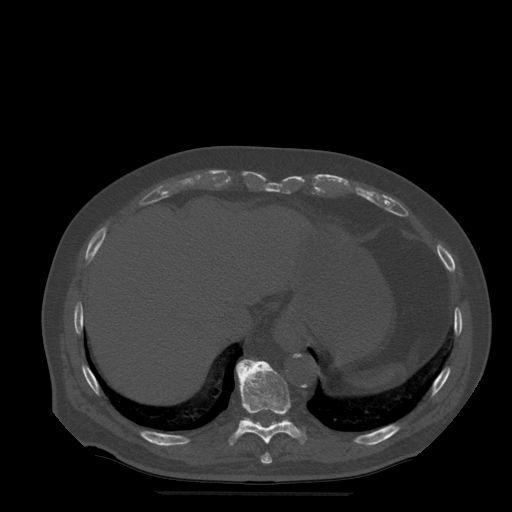
CT including the spine, one axial slice; position 265 of 522 along the scan axis; bone window (W 1800 / L 400 HU); 1.25 mm slice thickness; 512 × 512 image matrix, field of view 420 × 420 mm. Patient age 72 years. Case-level facts recorded for this patient, not image findings: primary cancer: prostate.
Outlined on this slice (semi-automatic segmentation, software-assisted and operator-edited):
- T10 vertebra: bounding box <229,360,307,446> (left, top, right, bottom; pixels)
- T11 vertebra: <248,360,275,423>
- T9 vertebra: <261,453,273,464>